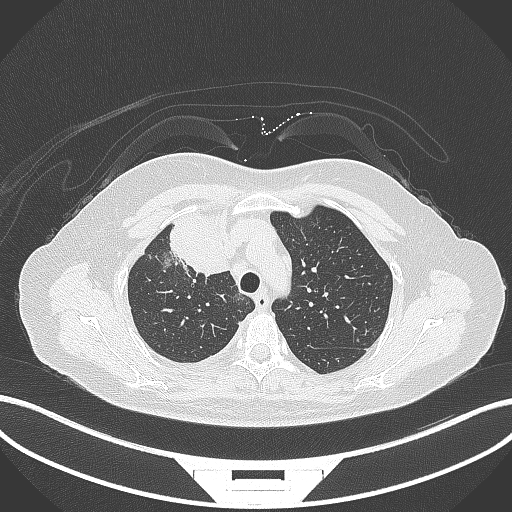
Chest CT, one axial slice. Position 231 of 305 along the scan axis. Reconstruction kernel B70f. 120 kVp. Lung window (W 1500 / L -600 HU). 512 × 512 image matrix, field of view 400 × 400 mm. Female patient, age 52 years. From the clinical record (not read from this slice): clinical TNM (as recorded): T3 N1 M1.
Outlined on this slice (rectangle marked by the reading radiologist):
- lung tumour (recorded histology: adenocarcinoma): bounding box (x1, y1, x2, y2) in pixels: (164, 211, 233, 279)